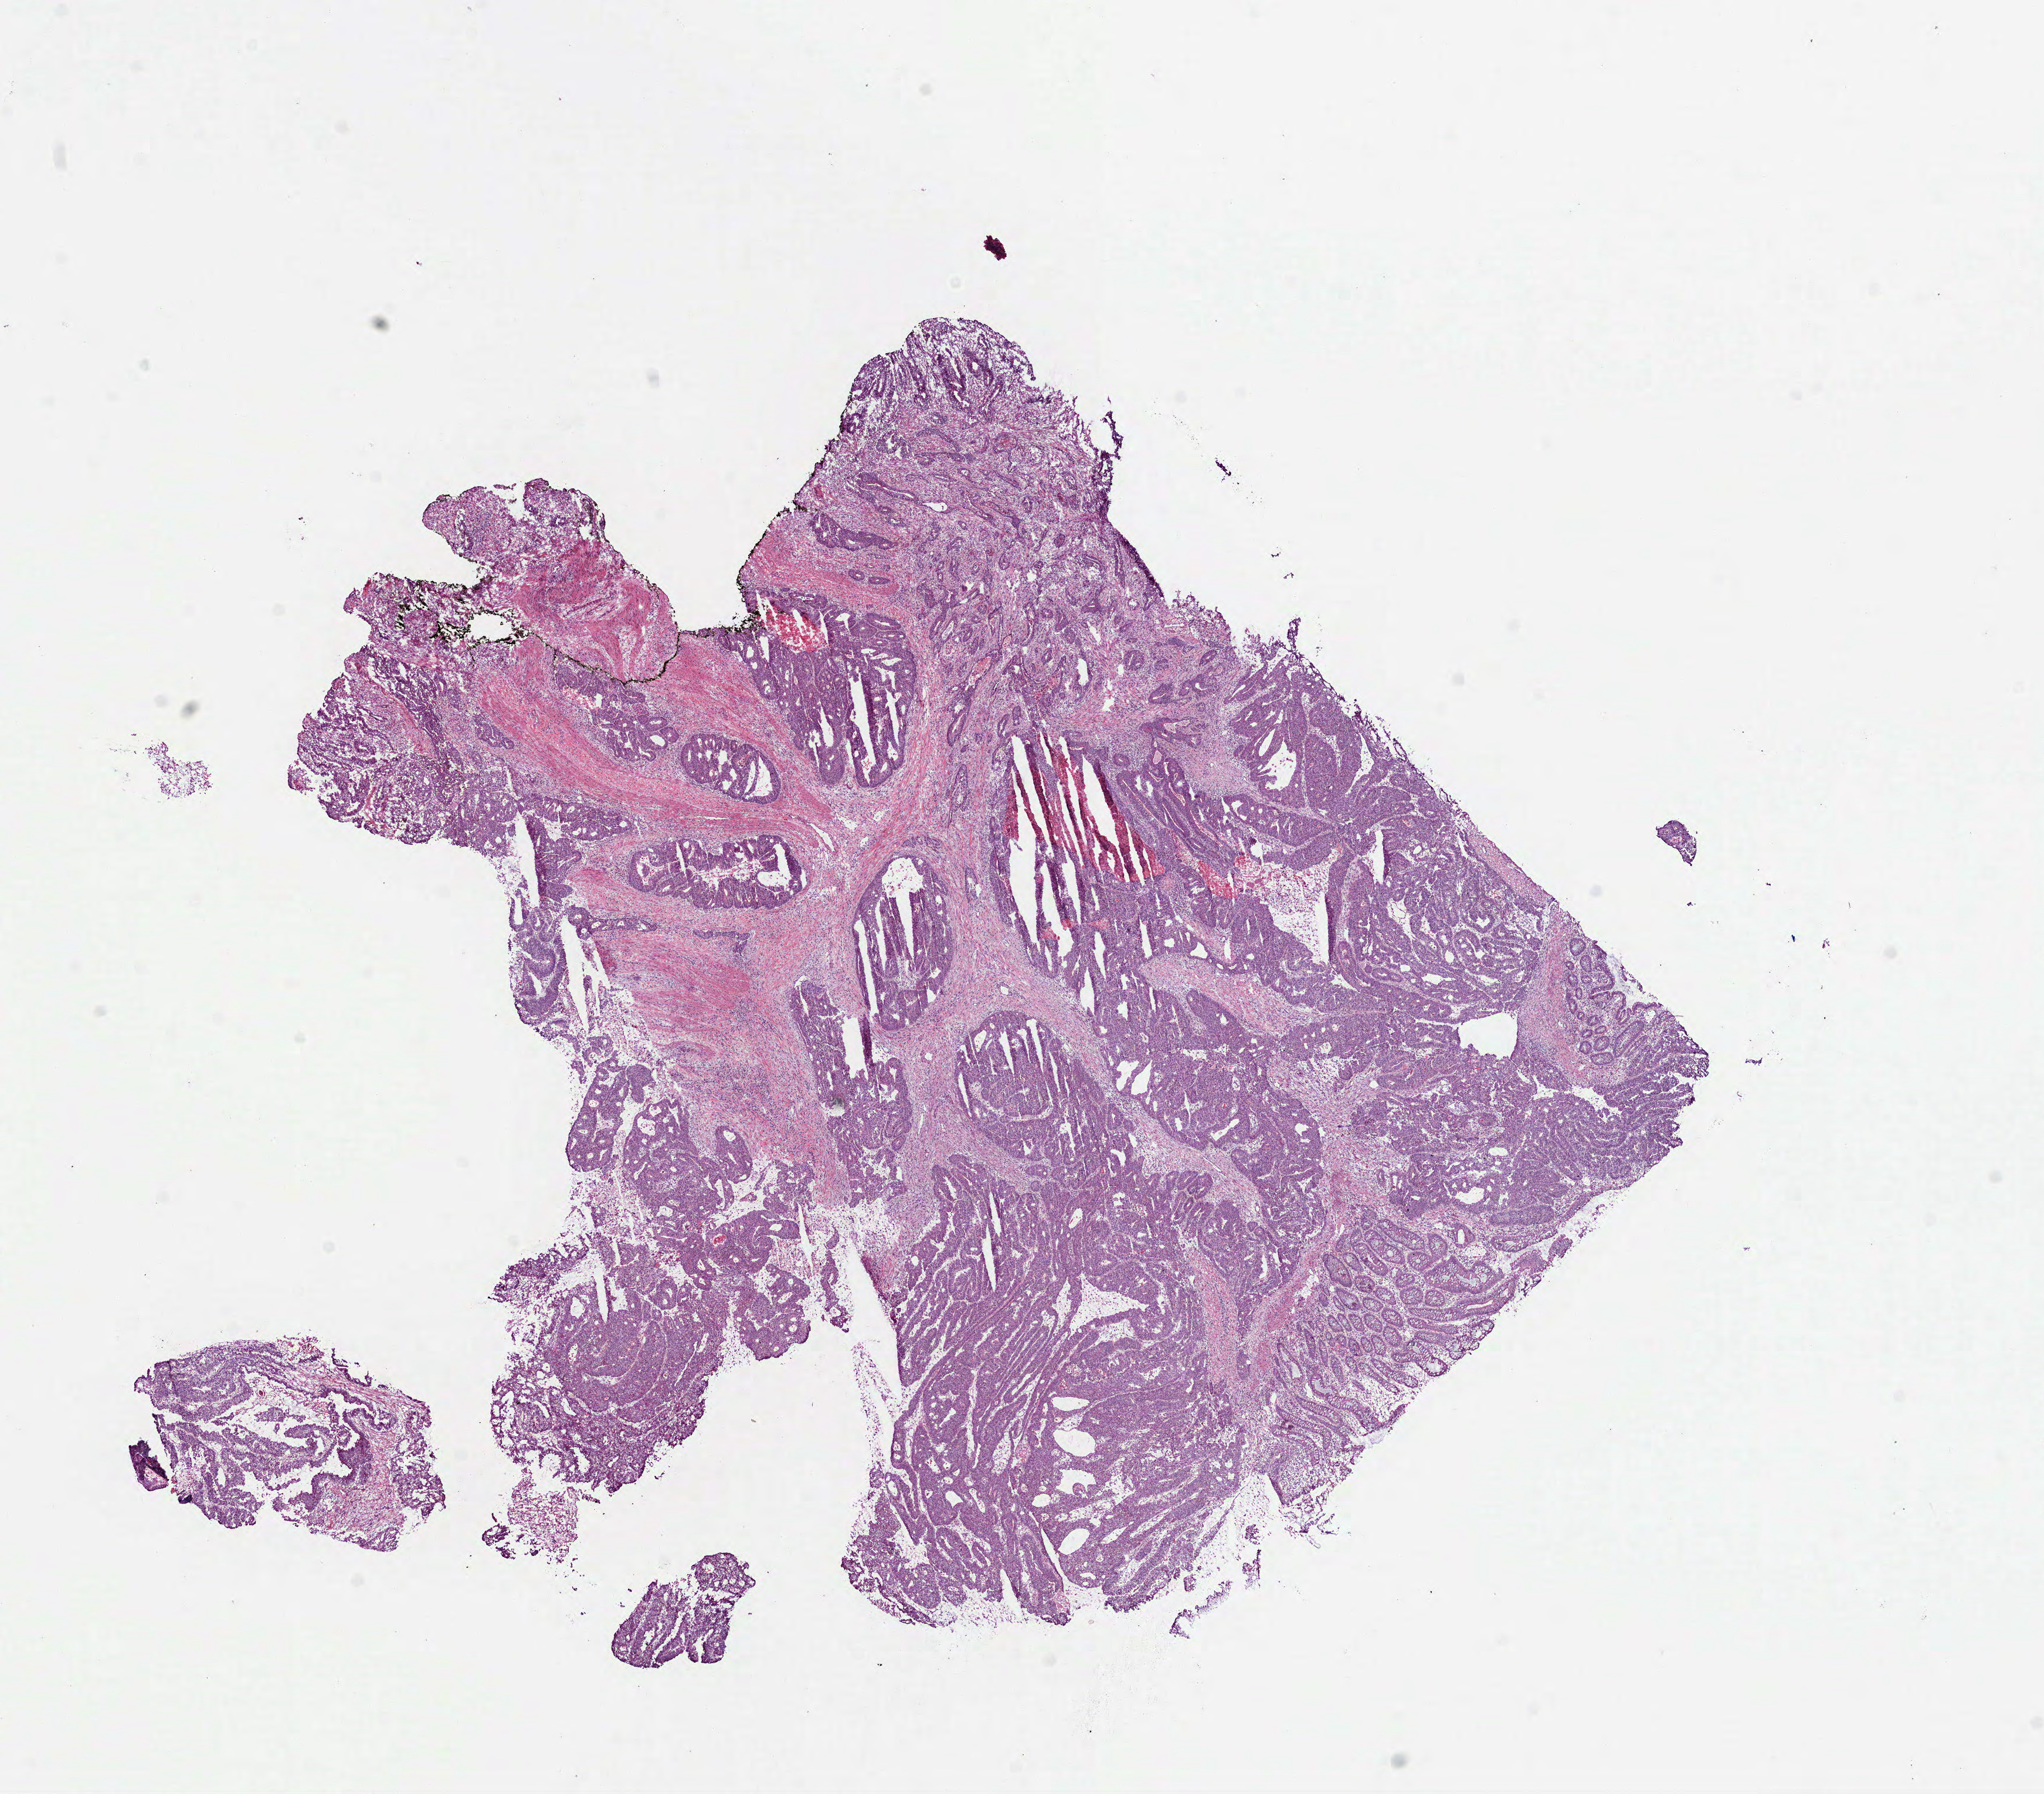
H&E whole-slide image, low-resolution overview of the scanned area, about 14.1 x 12.3 mm. Frozen section from the bottom of the tissue portion. Primary tumour sample from the colon. Patient: male, age at initial diagnosis 62 years. Composition of this section per pathologist review: tumour cells 95%, tumour nuclei 80%, normal cells 0%, stromal cells 0%, necrosis 5%. Infiltration values recorded for this section: lymphocyte infiltration 8%, monocyte infiltration 0%, neutrophil infiltration 7%.
Lymph nodes positive (case pathology): 0 of 46 examined. AJCC pathologic stage: IIA. Diagnosis: Adenocarcinoma, NOS (descending colon).